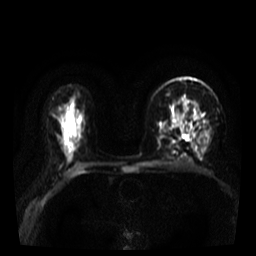
Breast MRI, one axial slice. Position 23 of 39 along the scan axis. Diffusion-weighted series; image 2 of 4 stored at this slice position (different b-values; order by instance number). 3 T. 5 mm slice thickness. 256 × 256 image matrix. Female patient.
Annotated regions visible in this slice (expert manual segmentation):
- tumour on diffusion-weighted imaging: box from (x=180, y=125) to (x=185, y=133) px